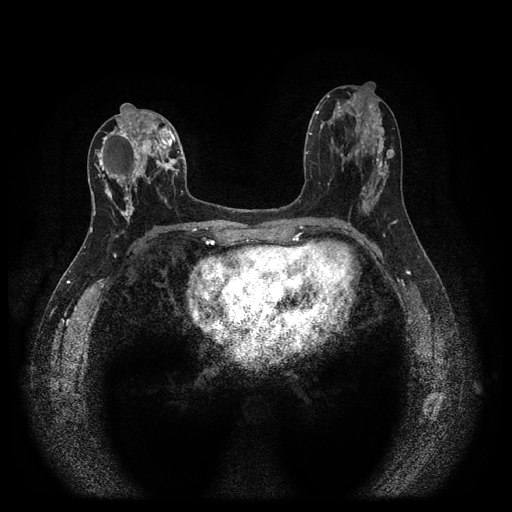
Breast MRI (dynamic contrast-enhanced, multi-phase), one axial slice; slice 49 of 116 in the series (ordered by position); dynamic contrast-enhanced series, time point 2 of 5 at this slice position (early post-contrast); 1.5 T; TE 2.7 ms, TR 5.4 ms; 2 mm slice thickness; 512 × 512 image matrix, field of view 330 × 330 mm. Patient: female, 47 years.
Annotated regions visible in this slice (semi-automatic segmentation, software-assisted and operator-edited):
- breast lesion (labelled benign in the annotation): box from (x=386, y=148) to (x=395, y=160) px
- breast lesion (labelled 'tumour' in the annotation; benign lesions carry a separate 'benign' label): (x=96, y=115)–(x=180, y=222)
- breast lesion (labelled benign in the annotation): (x=106, y=188)–(x=113, y=201)